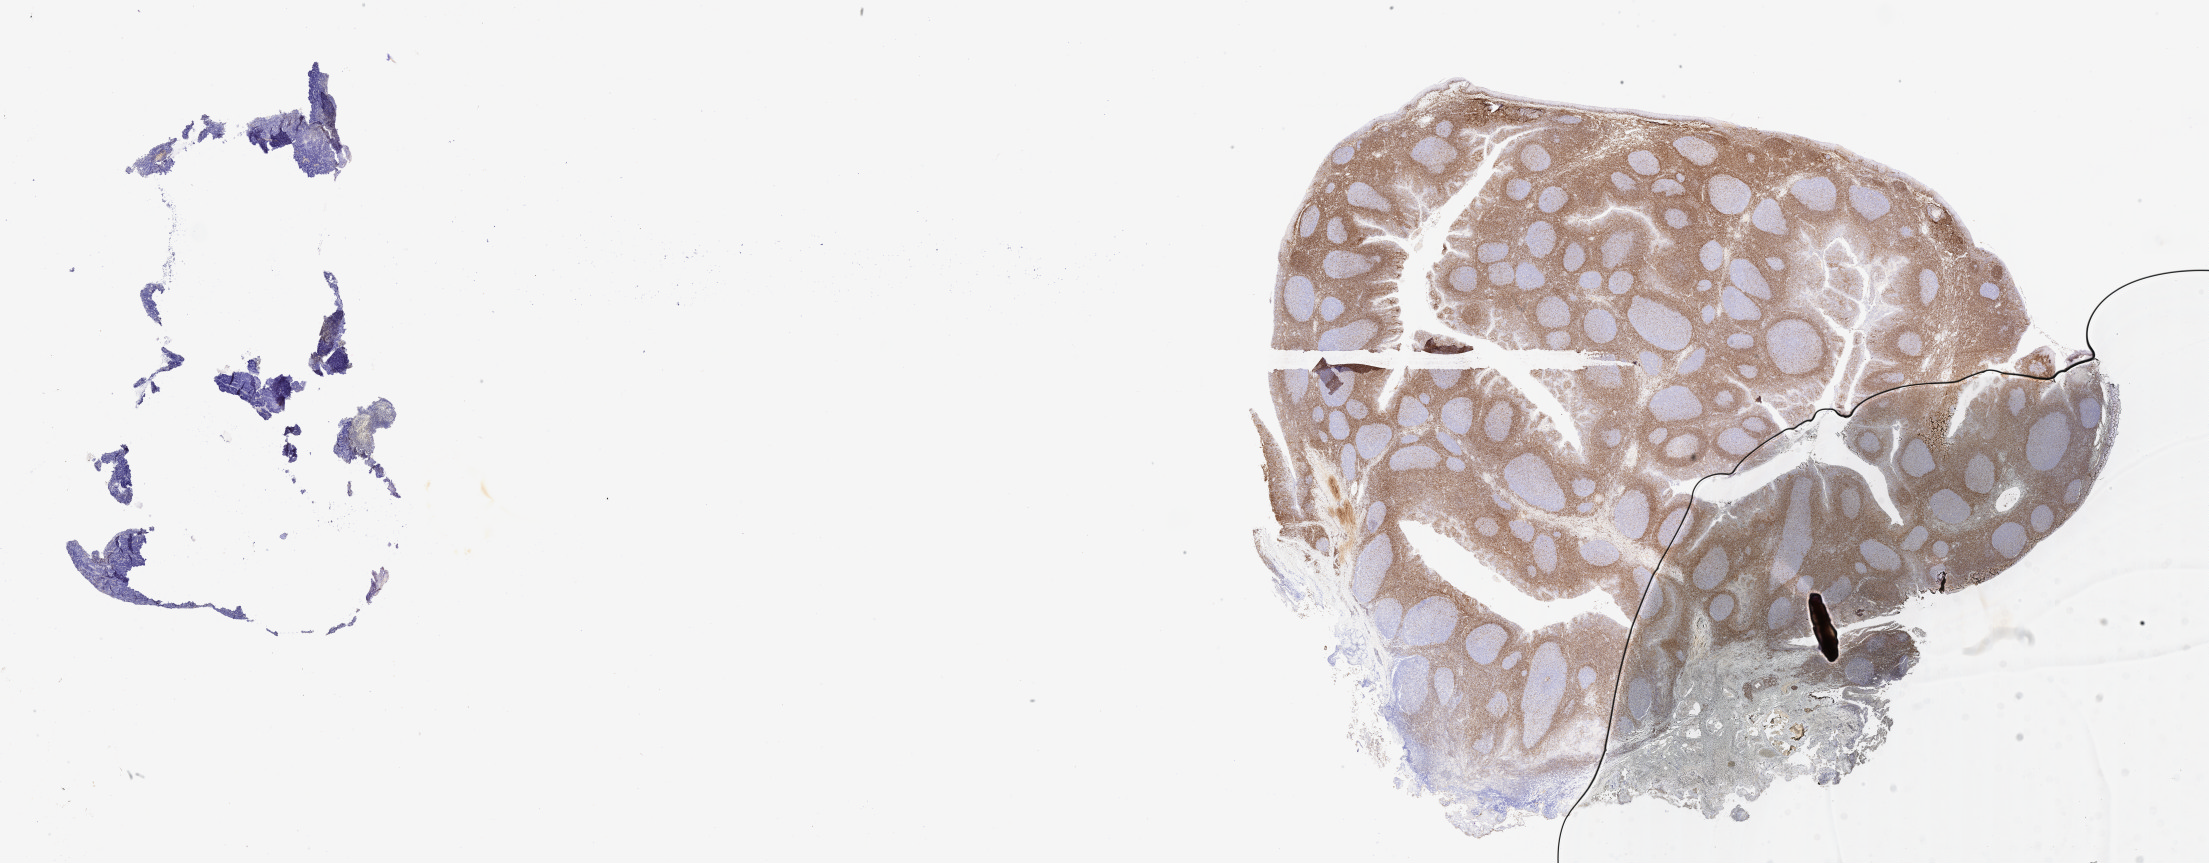
IHC for BCL2, whole-slide image — shown as a low-resolution overview of the whole scanned area (about 35.7 x 14.0 mm). Tumor tissue. Site: cranium. Patient: female, aged 10.
Histologic diagnosis: Burkitt lymphoma, NOS.